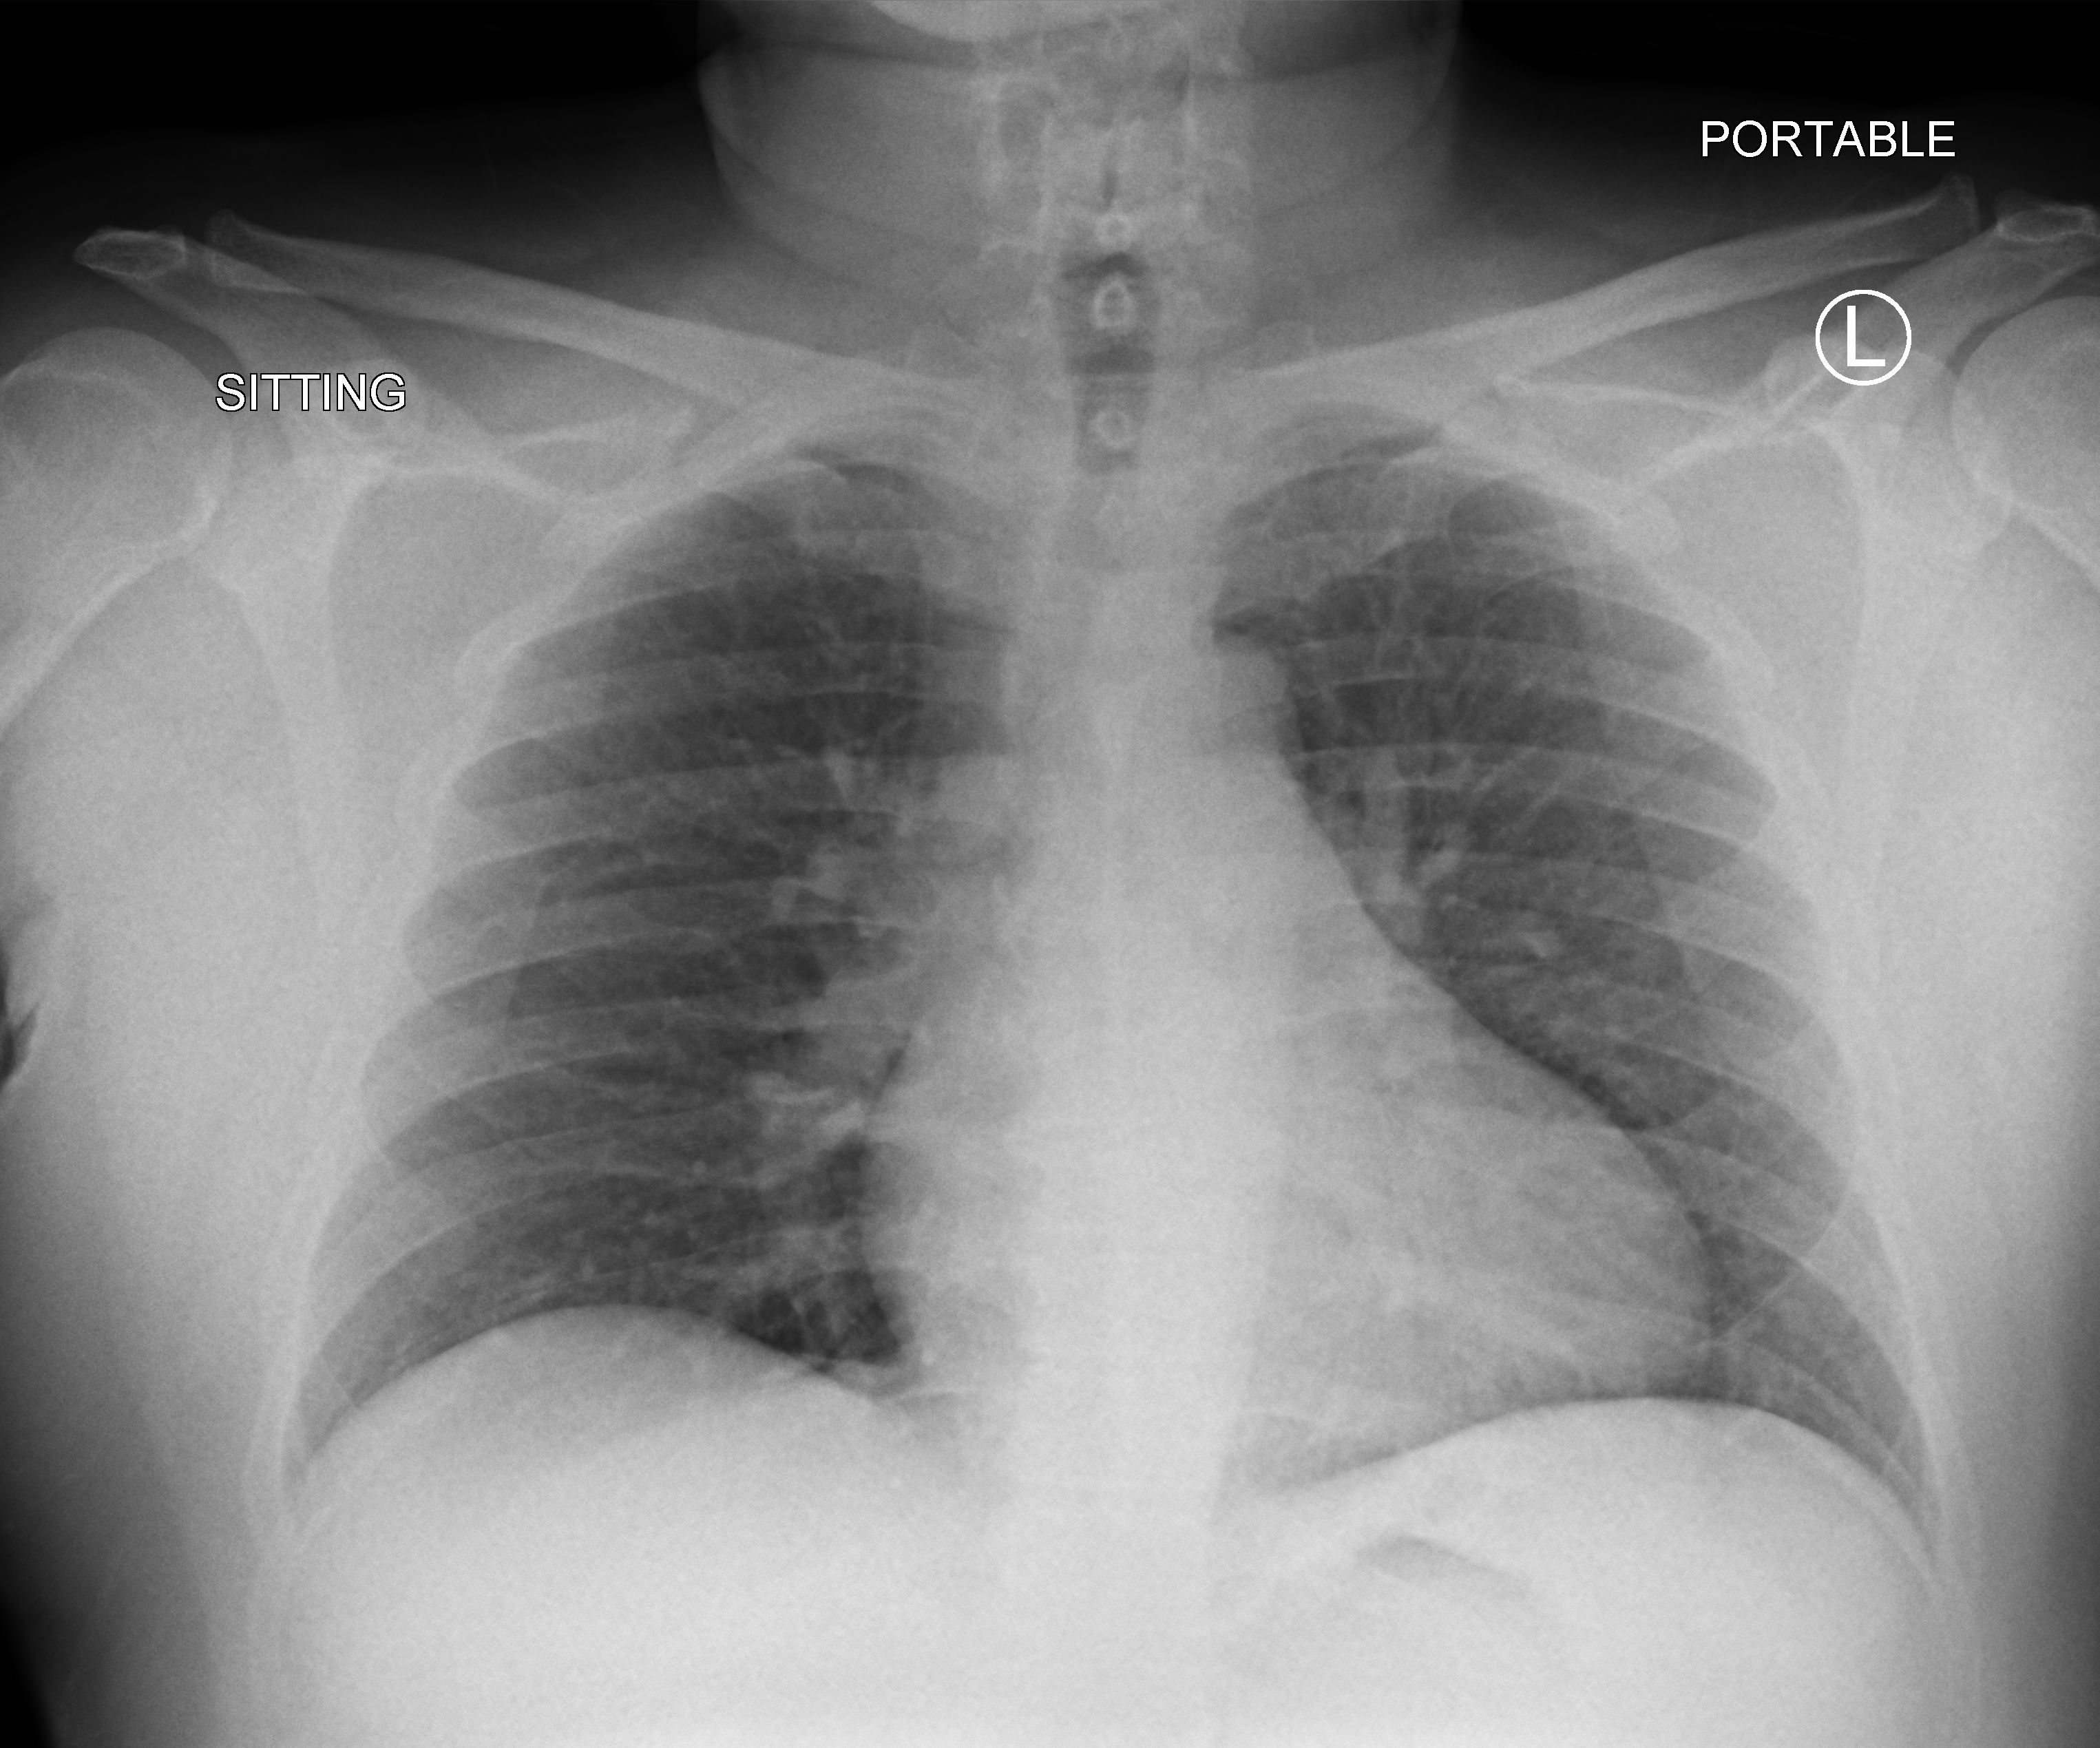
Portable chest radiograph; anteroposterior (AP) projection. Male patient hospitalised with COVID-19, age 18–59 years.
From the hospital-stay record, not from the radiograph (when in the stay this image was taken is not recorded): diabetes (admission record): no; length of hospital stay: 22 days; mechanically ventilated during this hospital stay: yes.